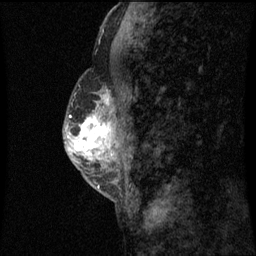
Breast MRI (dynamic contrast-enhanced), one sagittal slice. Slice 27 of 60 in the series (ordered by position). Dynamic contrast-enhanced series, image 2 of 3 at this slice position (ordered by acquisition). 1.5 T. TE 4.2 ms, TR 8.9 ms. 2 mm slice thickness. 256 × 256 image matrix, field of view 200 × 200 mm. Patient: female, 50 years. From the clinical record (not read from this slice): setting: breast cancer imaged before/during neoadjuvant chemotherapy; receptor status: triple-negative.
Outlined on this slice (semi-automatically segmented with operator editing):
- analysis volume of interest (the breast-tissue region the enhancement analysis was run in; not a lesion): bounding box <68,82,114,169> (left, top, right, bottom; pixels)
- tumour enhancement mask (voxels above the 70 % enhancement threshold inside the analysis volume of interest): <68,96,111,157>